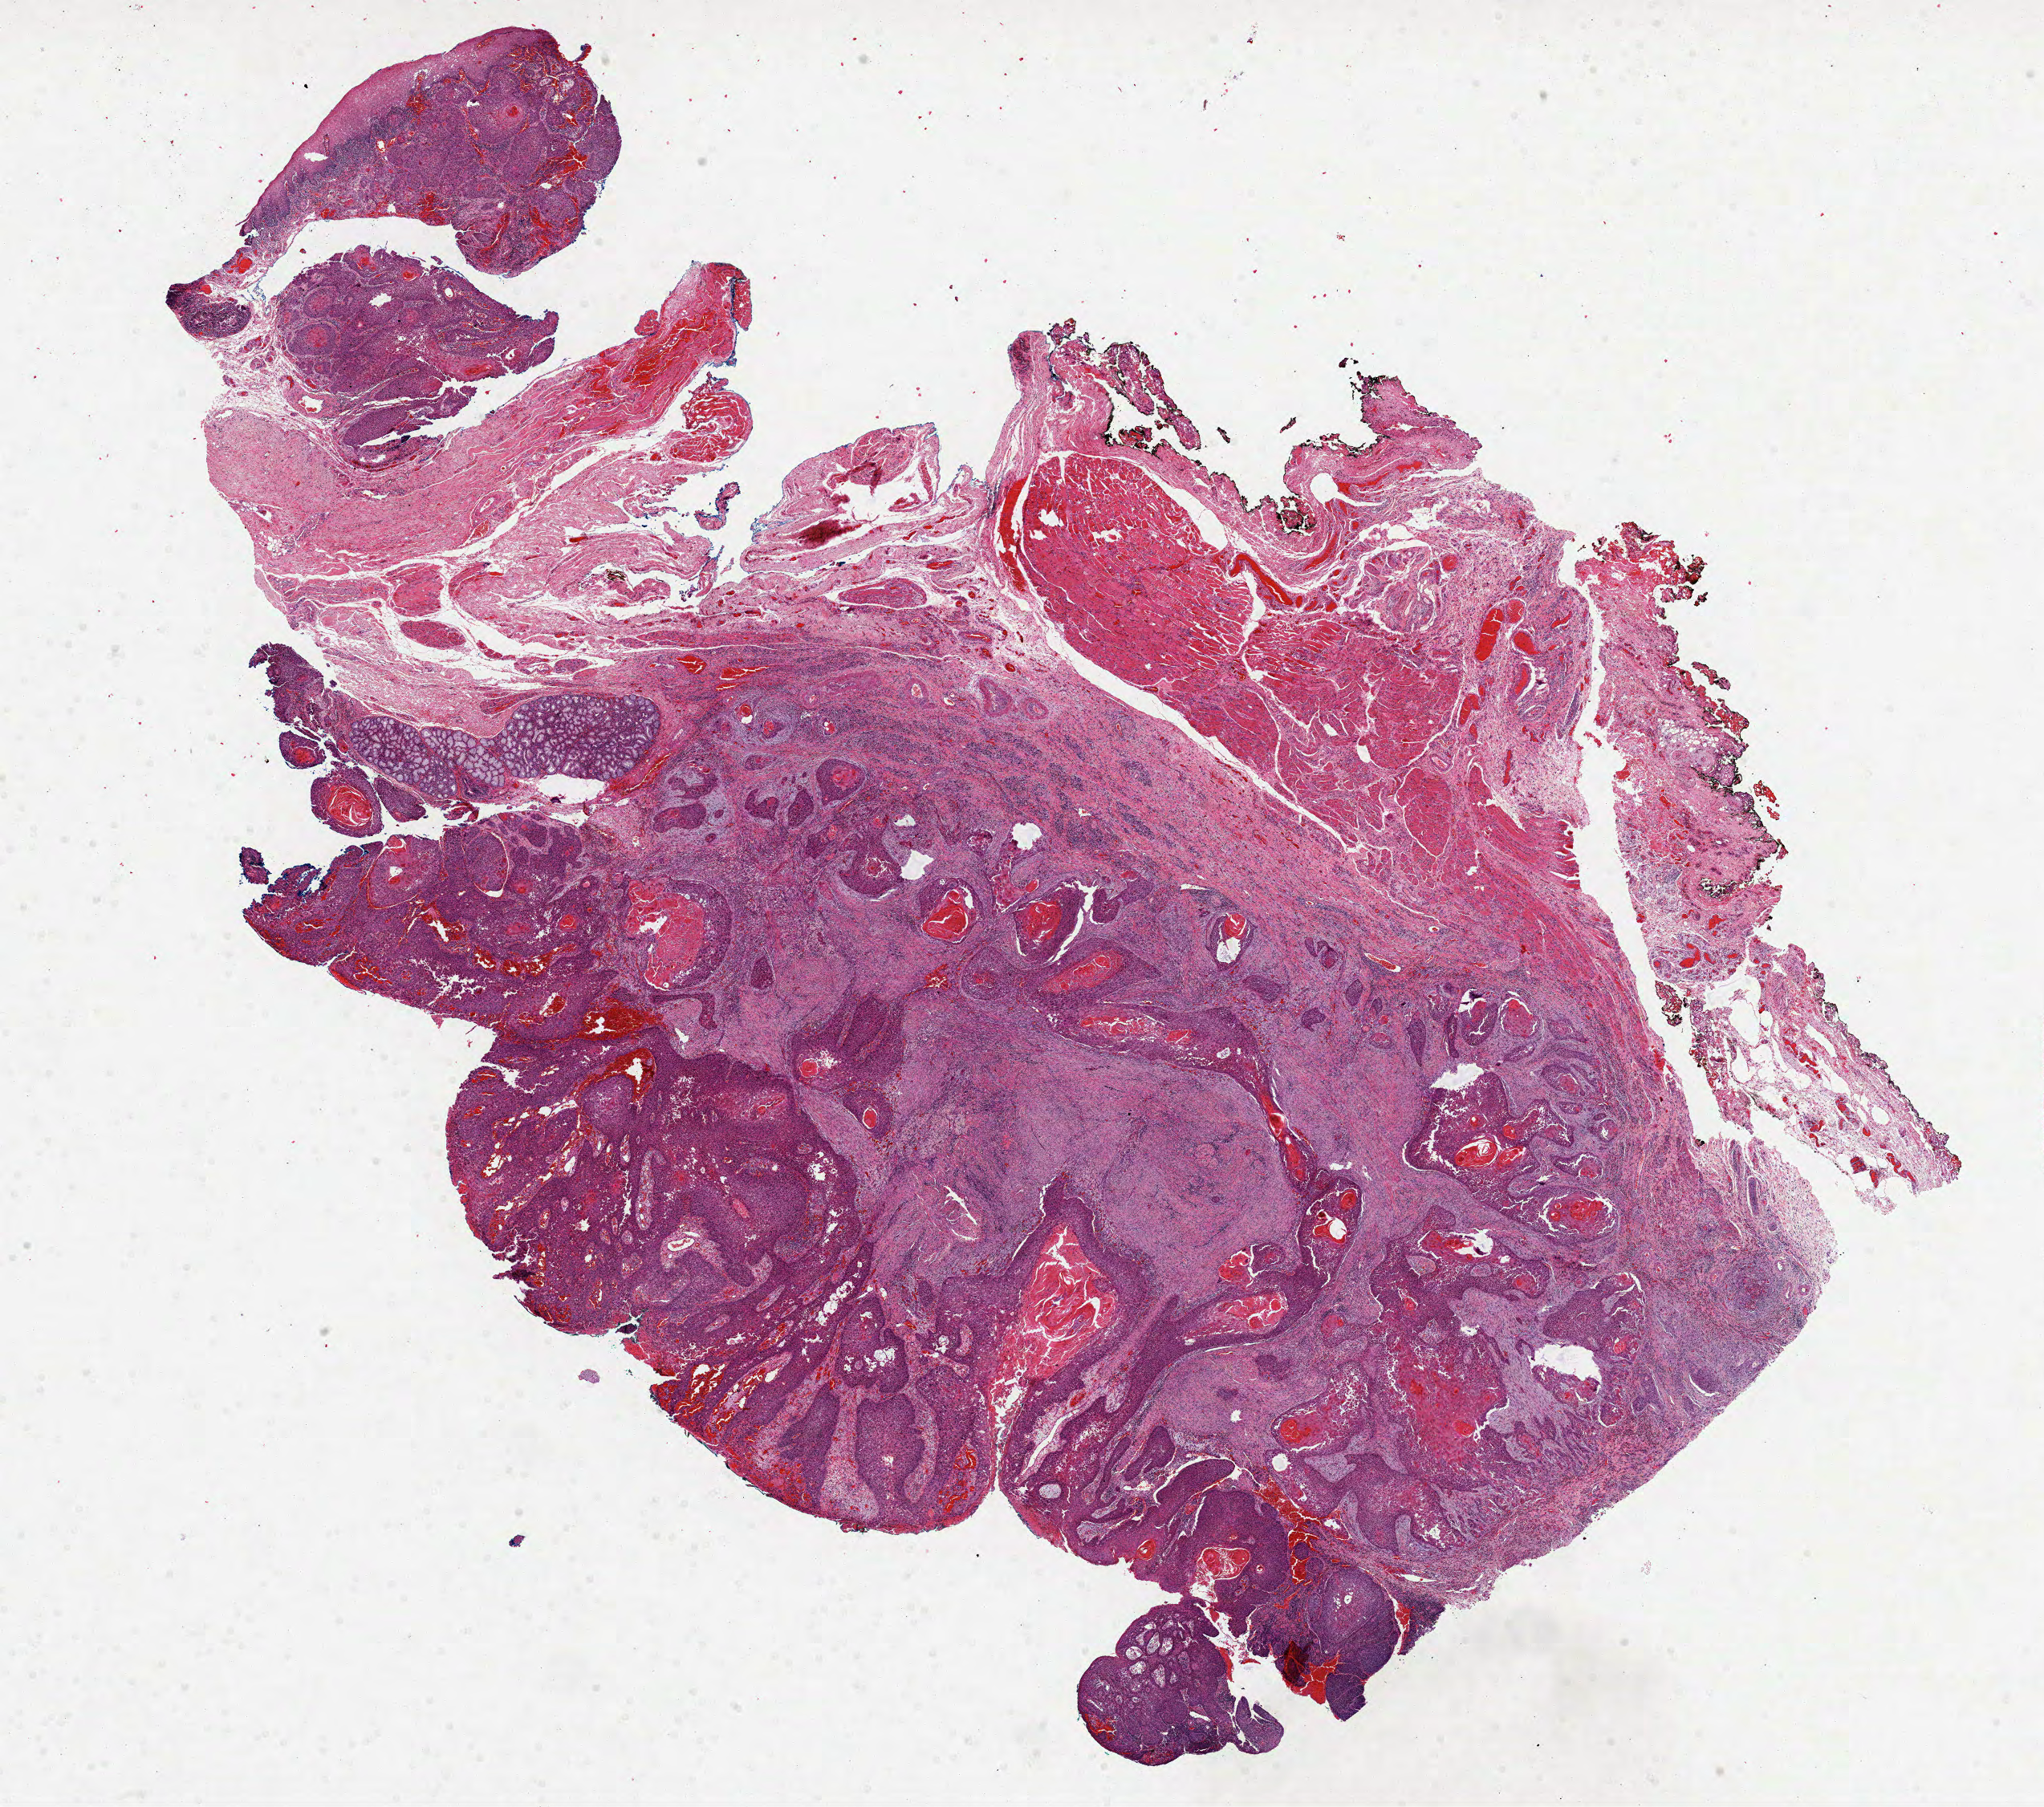
H&E-stained whole-slide image — shown as a low-resolution overview of the whole scanned area (about 20.5 x 18.2 mm), formalin-fixed paraffin-embedded (FFPE) diagnostic section, primary tumour sample from the head and neck. Patient: male, age at initial diagnosis 62 years. Histologic grade: G2 (moderately differentiated).
Diagnosis: Squamous cell carcinoma, NOS. AJCC pathologic stage: I. Laterality: left. TNM: T1 N0.